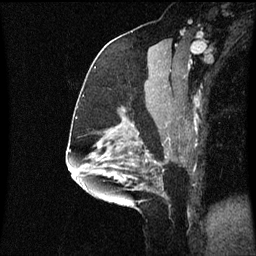
Breast MRI (dynamic contrast-enhanced), one sagittal slice; position 34 of 60 along the scan axis; dynamic contrast-enhanced series, image 2 of 3 at this slice position (ordered by acquisition); 1.5 T; TE 4.2 ms, TR 8.9 ms; 256 × 256 image matrix, field of view 200 × 200 mm. Patient: female, 58 years. From the clinical record (not read from this slice): setting: breast cancer imaged before/during neoadjuvant chemotherapy; receptor status: triple-negative.
Structures marked on this image (semi-automatically segmented with operator editing):
- analysis volume of interest (the breast-tissue region the enhancement analysis was run in; not a lesion): bounding box [x1, y1, x2, y2] px = [104, 118, 171, 179]
- tumour enhancement mask (voxels above the 70 % enhancement threshold inside the analysis volume of interest): [114, 162, 157, 179]